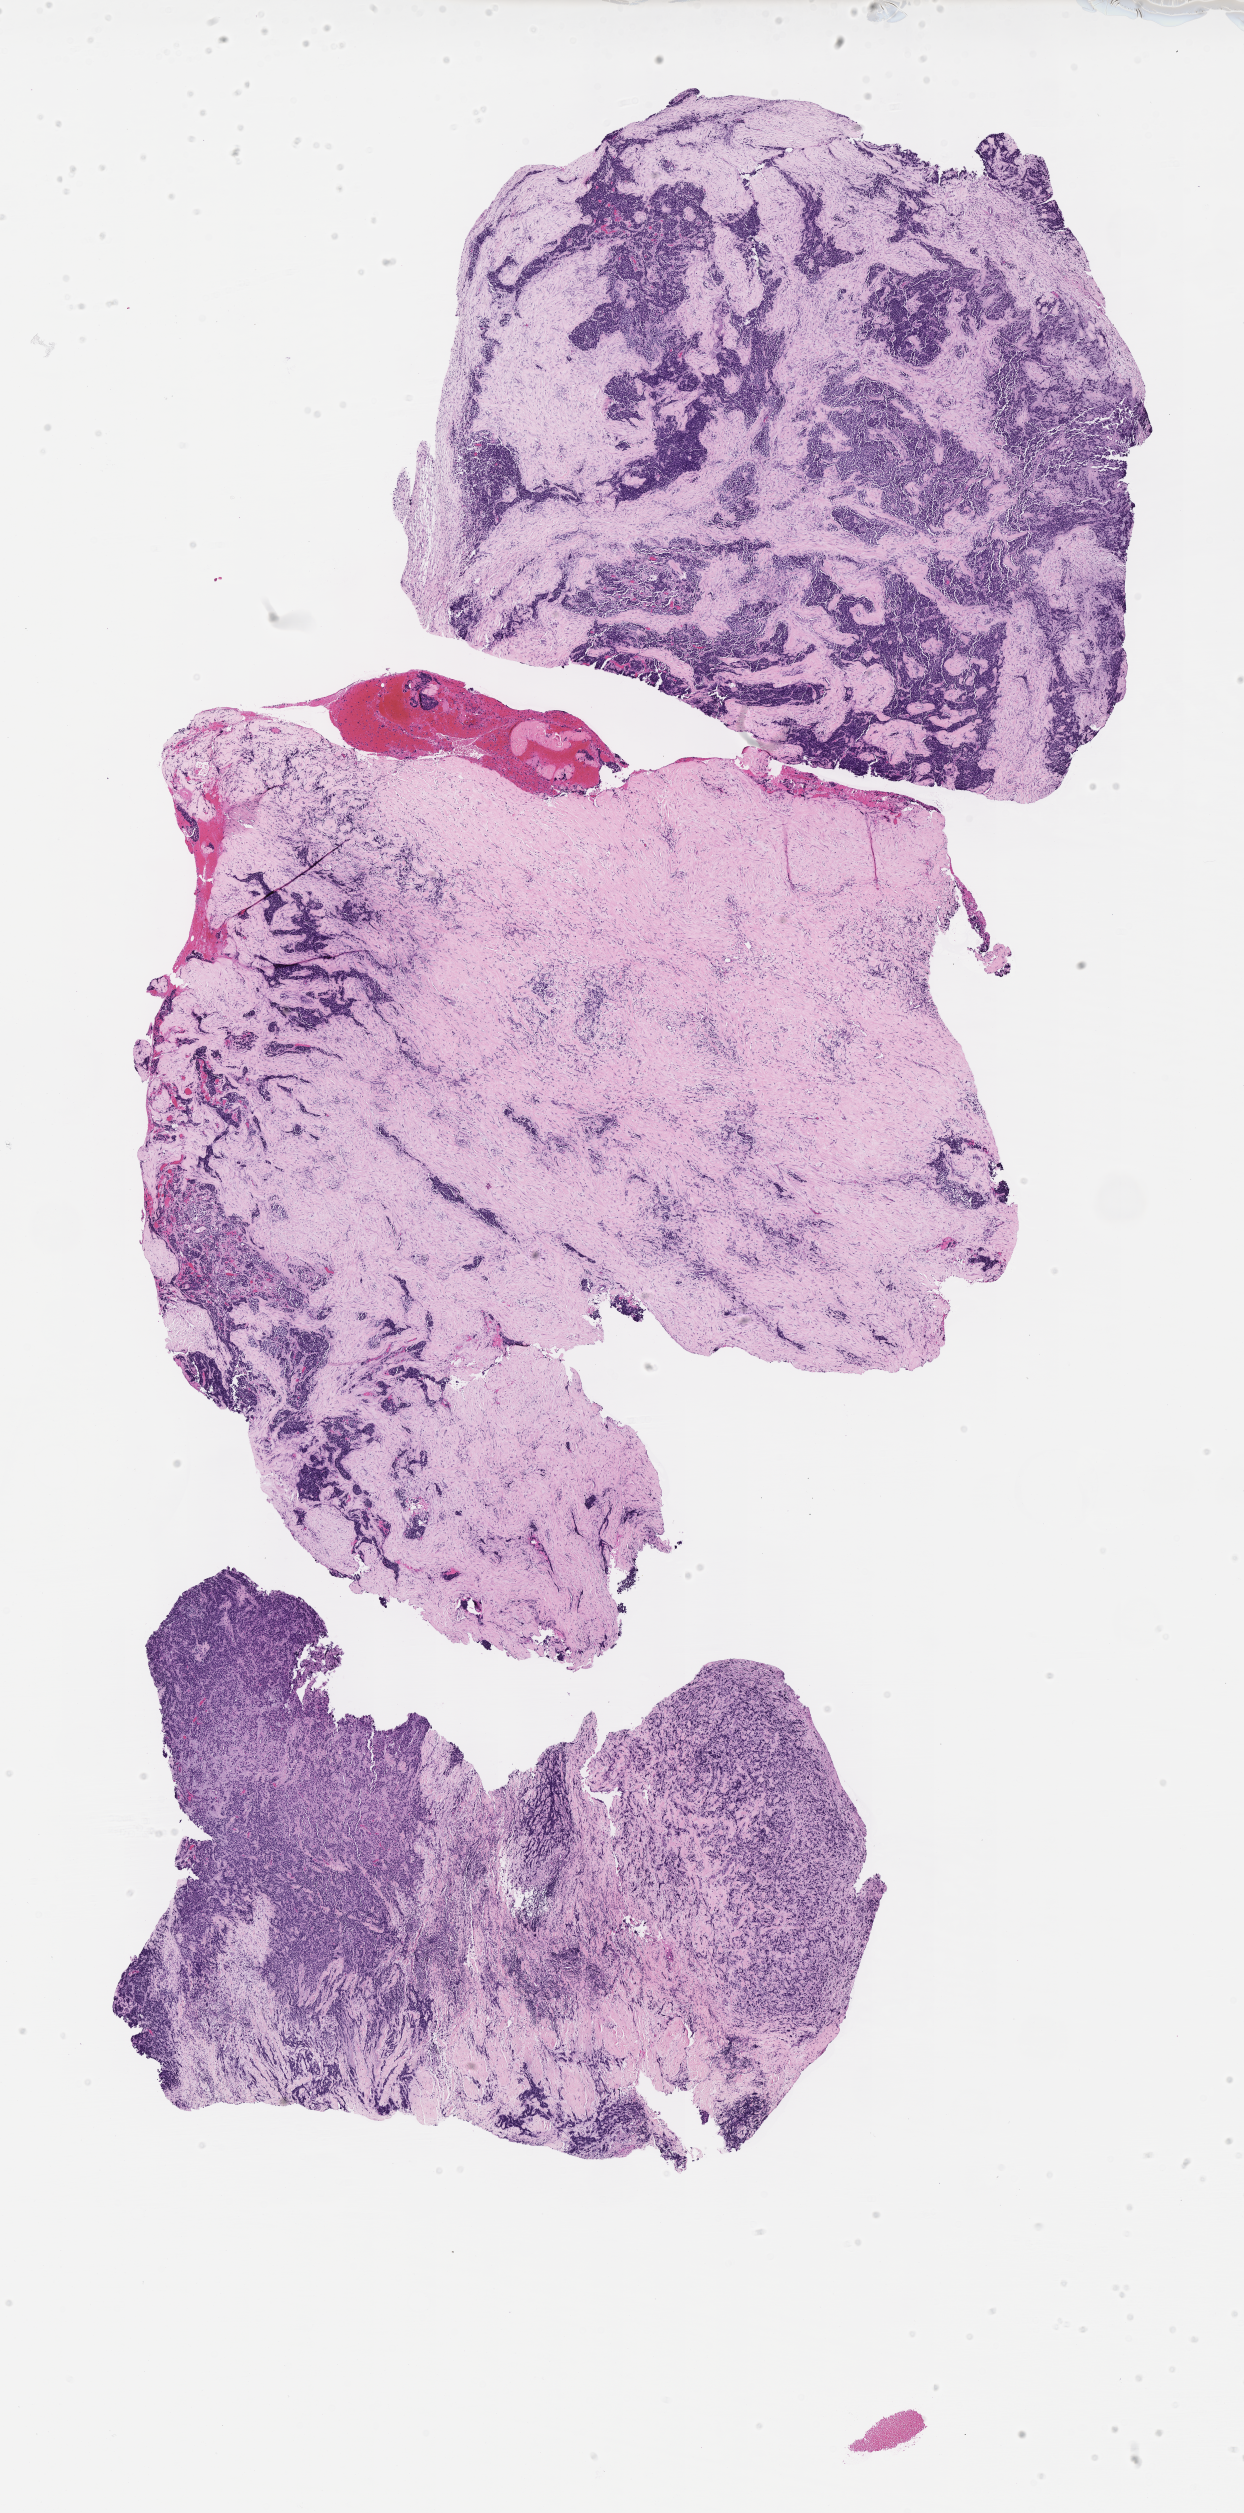
Digitized hematoxylin and eosin (H&E)-stained section of tumor tissue, shown as a low-resolution overview of the whole scanned area (about 10.1 x 20.3 mm); formalin-fixed paraffin-embedded section; sample anatomic site: mediastinum-left. Patient: female, age 10.5 years at diagnosis.
Stage (as recorded): 4. Metastatic status at presentation (as recorded): metastatic (confirmed). Diagnosis: rhabdomyosarcoma; histological classification: alveolar rhabdomyosarcoma.